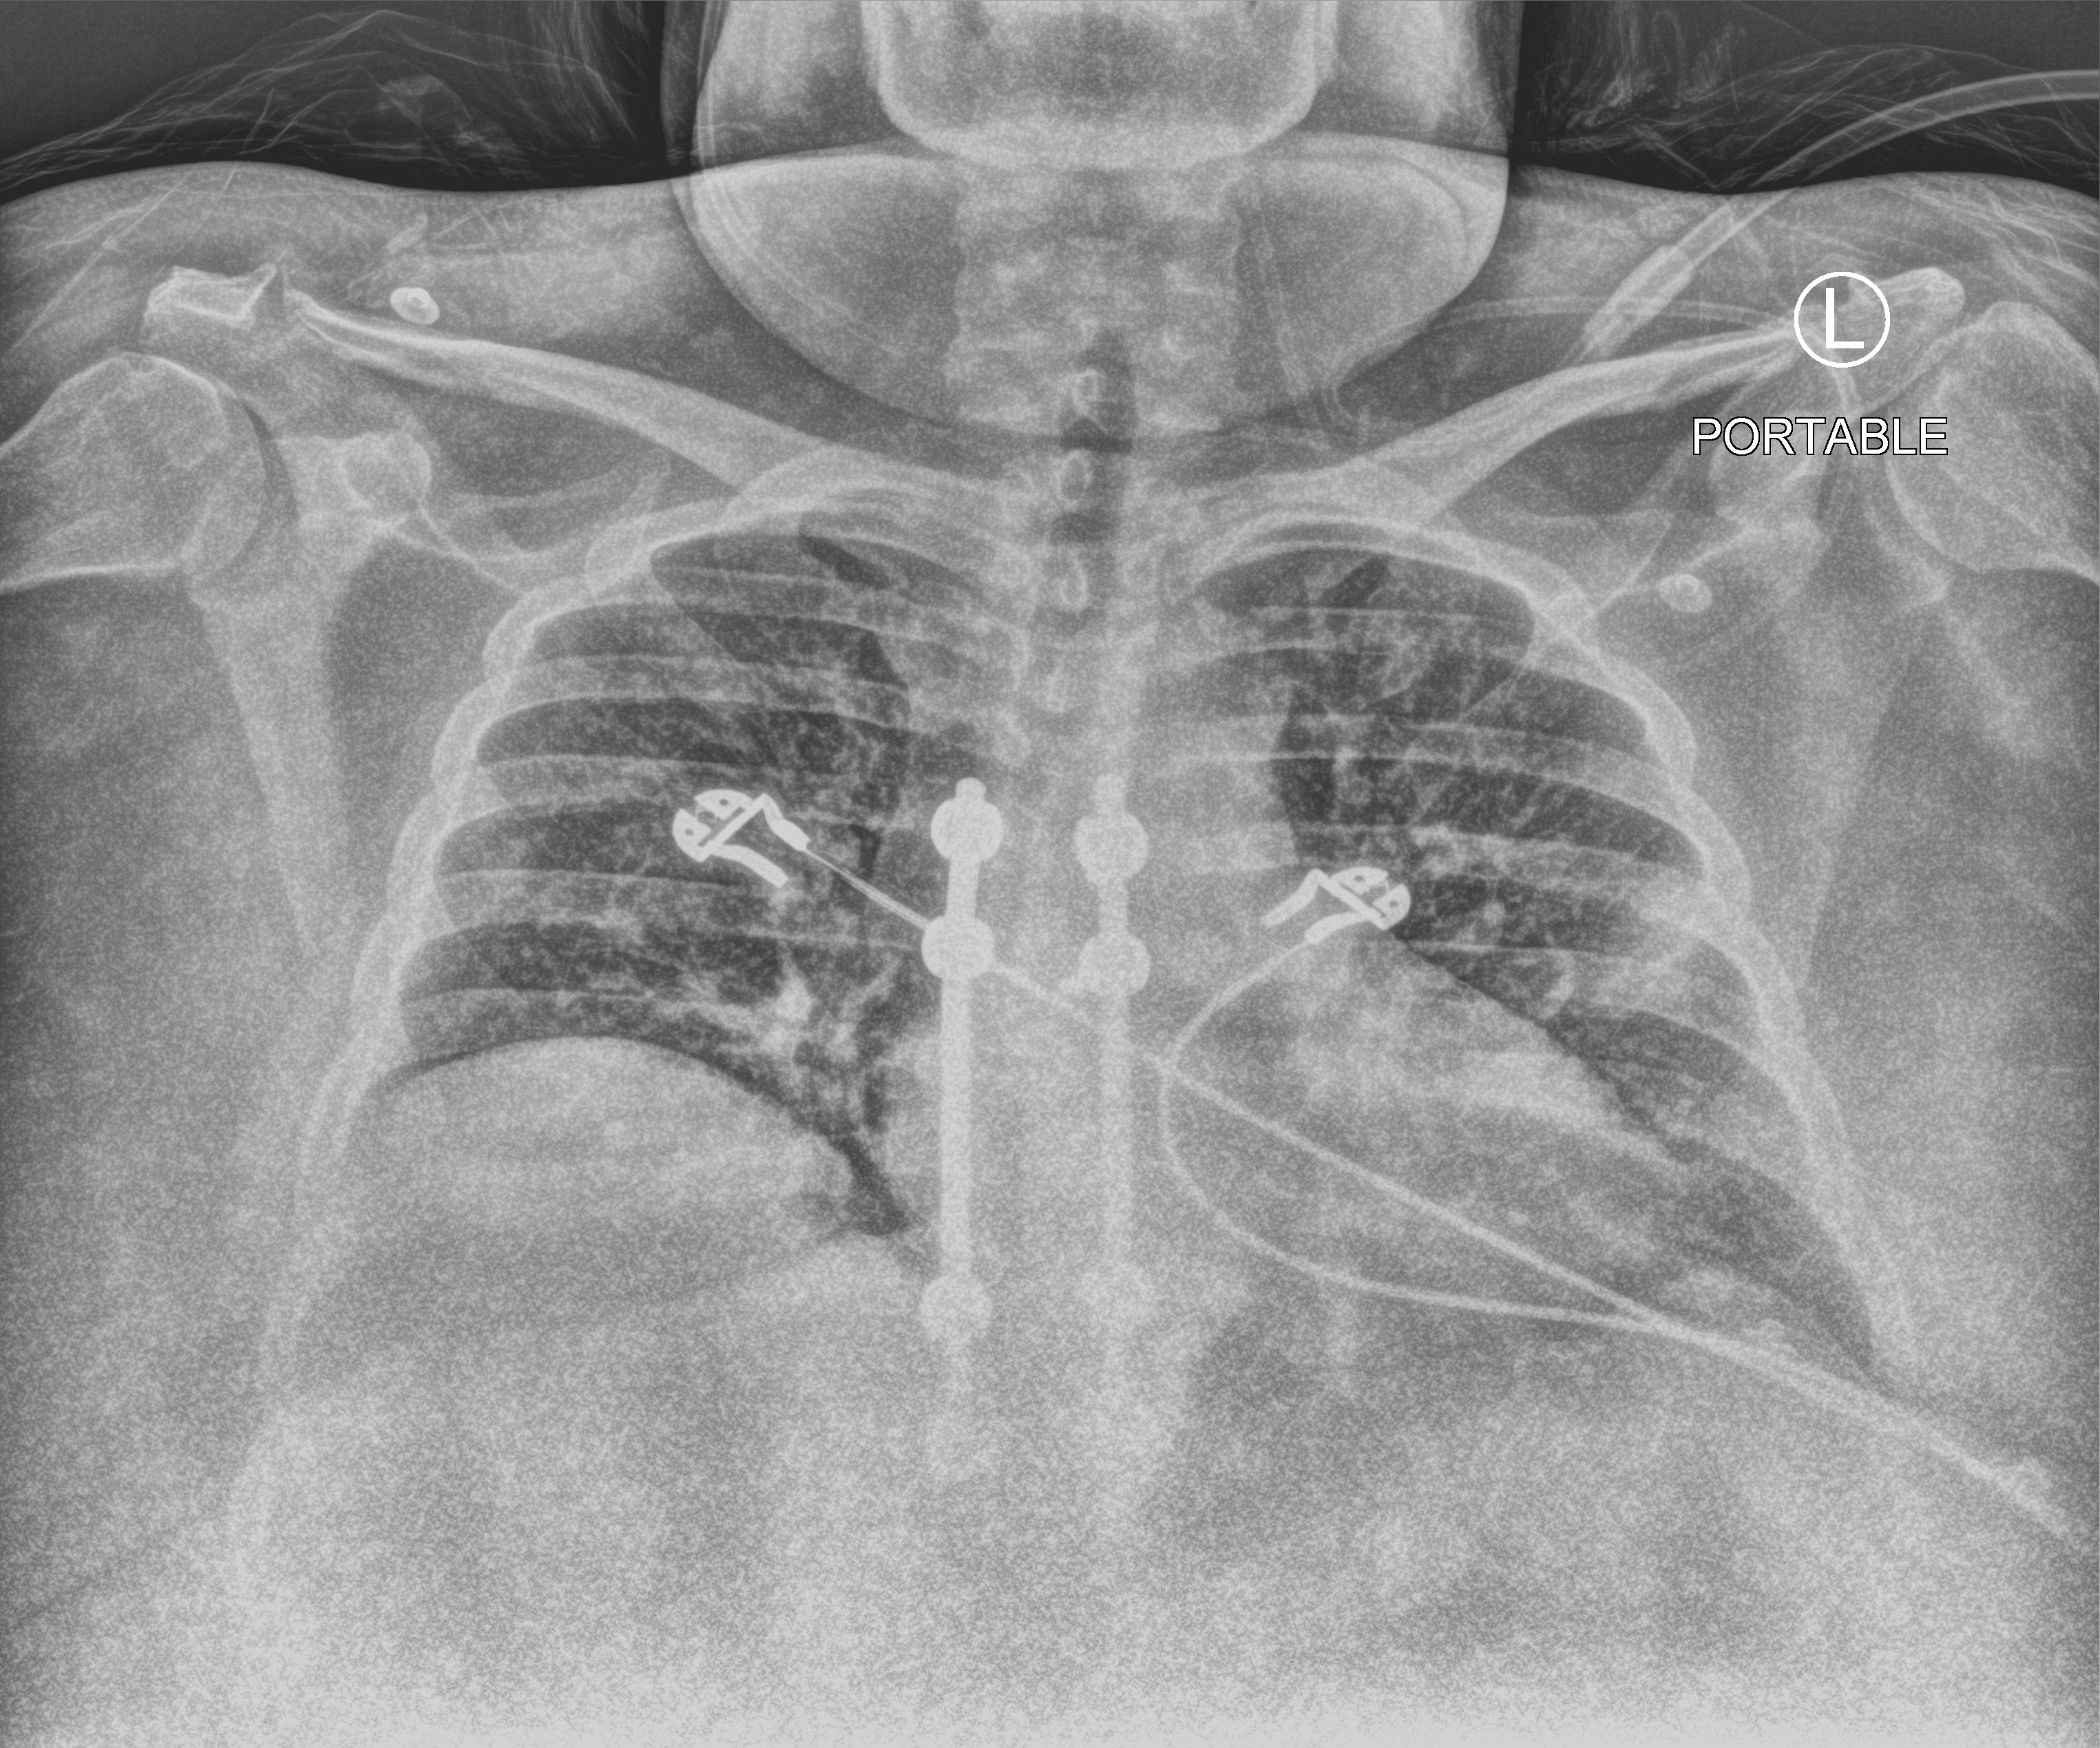
Chest X-ray (portable). Female patient hospitalised with COVID-19, age 18–59 years.
From the hospital-stay record, not from the radiograph (when in the stay this image was taken is not recorded):
- mechanically ventilated during this hospital stay: no
- admitted to intensive care during this hospital stay: no